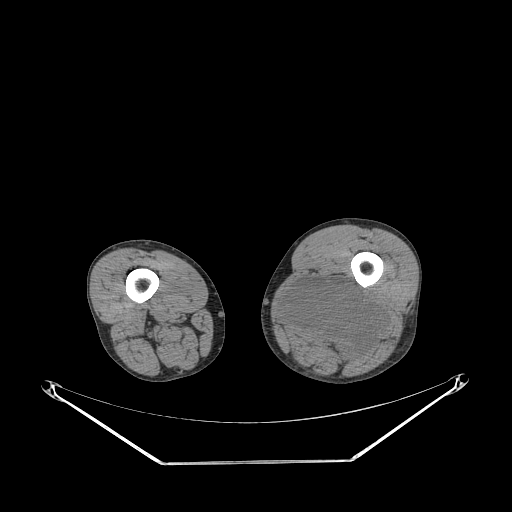
CT of an extremity soft-tissue mass (from a PET/CT study), one axial slice. Position 219 of 267 along the scan axis. 140 kVp. Soft-tissue window (W 400 / L 40 HU). 512 × 512 image matrix, field of view 500 × 500 mm. Male patient. From the clinical record (not read from this slice): histological type: undifferentiated pleomorphic liposarcoma; grade: high; site of the primary tumour: left thigh.
Annotated regions visible in this slice (expert contour drawn on MRI and transferred to this co-registered scan by the dataset authors):
- gross tumour volume including surrounding oedema: bounding box [x1, y1, x2, y2] px = [283, 276, 385, 359]
- gross tumour volume (mass): [283, 278, 385, 359]